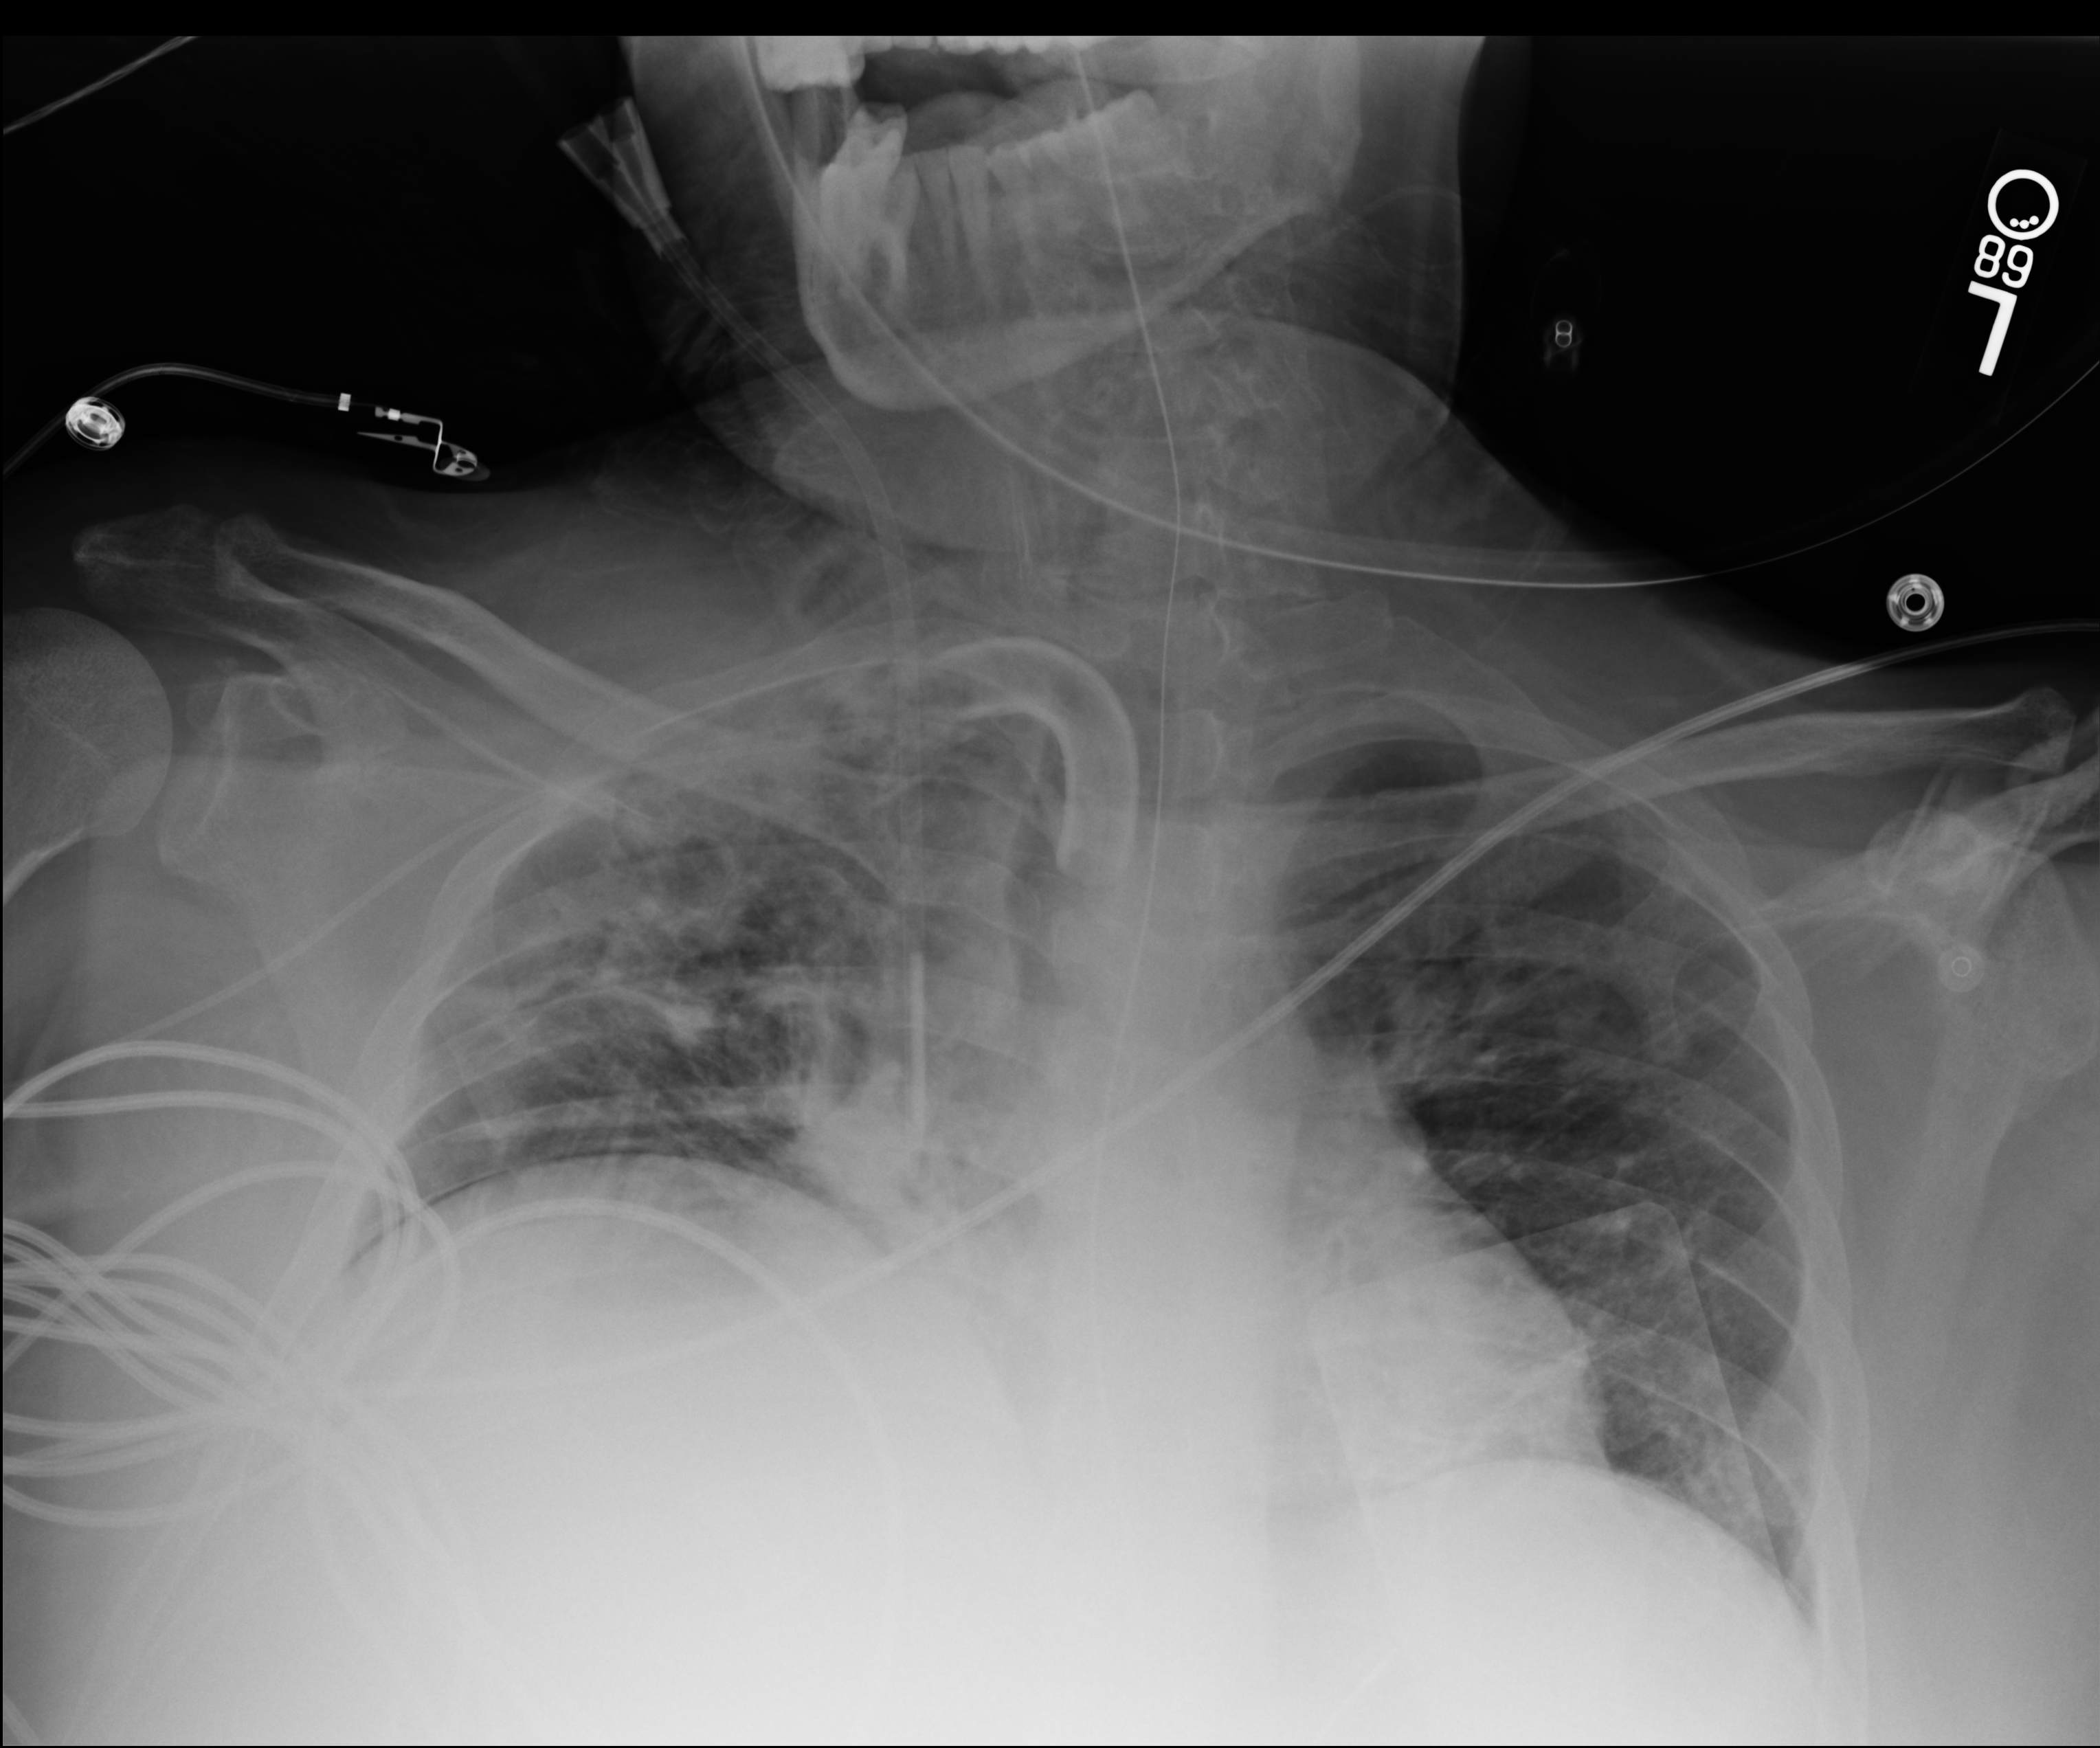
Portable chest radiograph. Patient hospitalised with COVID-19, aged 18–59 years.
From the hospital-stay record, not from the radiograph (when in the stay this image was taken is not recorded):
- mechanically ventilated during this hospital stay: yes